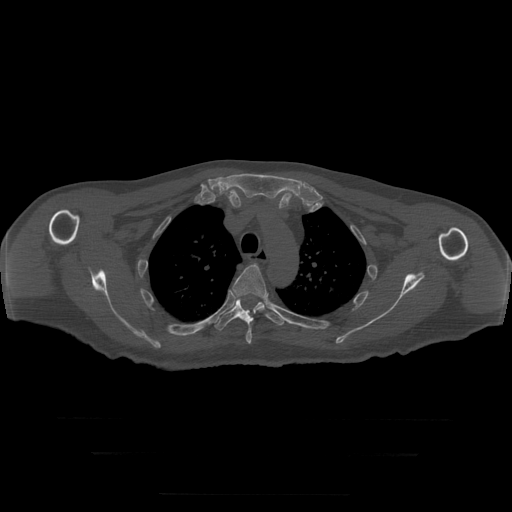
CT including the spine, one axial slice; reconstruction kernel STANDARD; bone window (W 1800 / L 400 HU); 1.25 mm slice thickness; 512 × 512 image matrix, field of view 510 × 510 mm. Patient age 73 years. Case-level facts recorded for this patient, not image findings: primary cancer: prostate.
Annotated regions visible in this slice (semi-automatic segmentation, software-assisted and operator-edited):
- T4 vertebra: bounding box (x1, y1, x2, y2) in pixels: (232, 265, 268, 344)
- T5 vertebra: (215, 299, 285, 331)